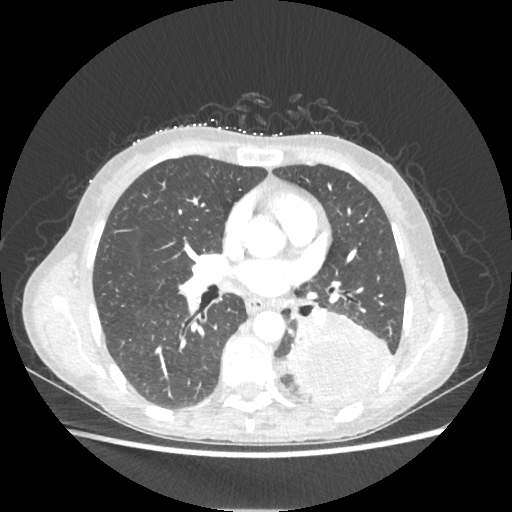
Chest CT, one axial slice; position 114 of 221 along the scan axis; reconstruction kernel STANDARD; 80 kVp; lung window (W 1500 / L -600 HU); 512 × 512 image matrix. Female patient, age 53 years. From the clinical record (not read from this slice): clinical TNM (as recorded): T3 N0 M0.
Annotated regions visible in this slice (bounding box drawn by a radiologist):
- lung tumour (recorded histology: adenocarcinoma): bounding box (x1, y1, x2, y2) in pixels: (287, 314, 391, 403)